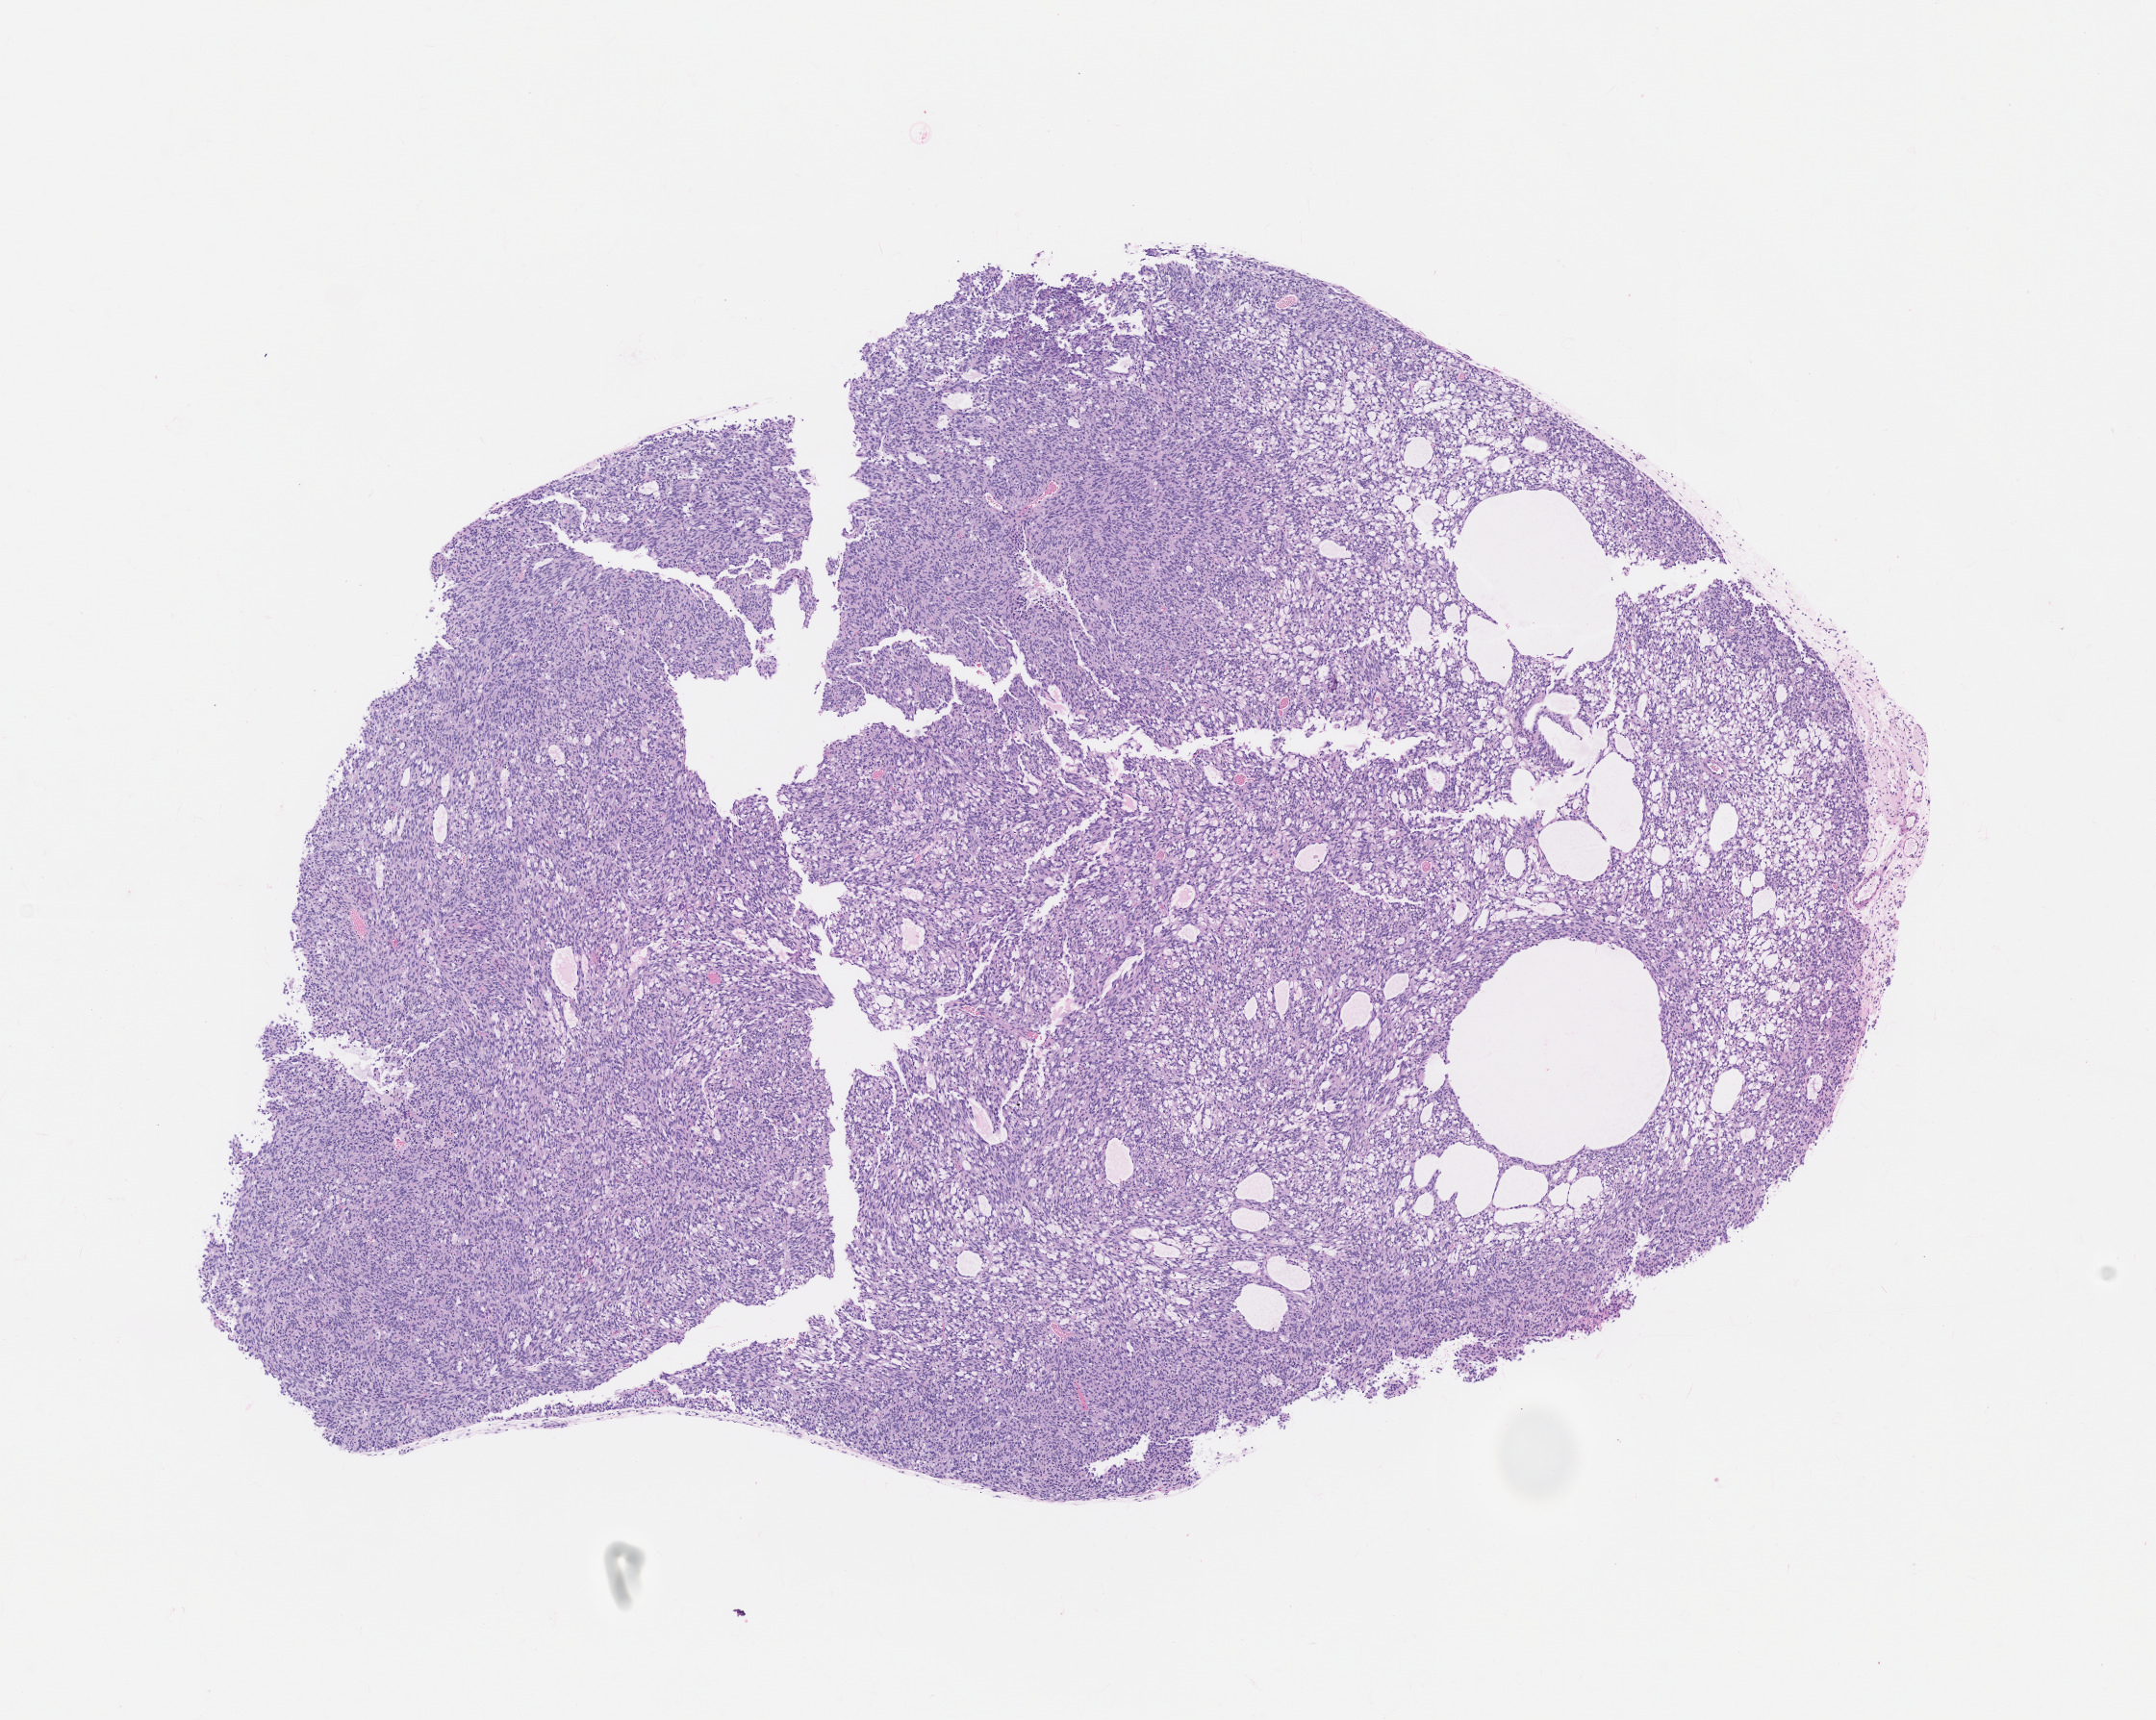
Whole-slide image, hematoxylin and eosin (H&E): patient-derived xenograft (human tumor grown in a mouse), passage 1, low-resolution overview of the scanned area, about 9.0 x 7.2 mm. FFPE section. Tumor site category: uterus.
• originating patient diagnosis: Leiomyosarcoma